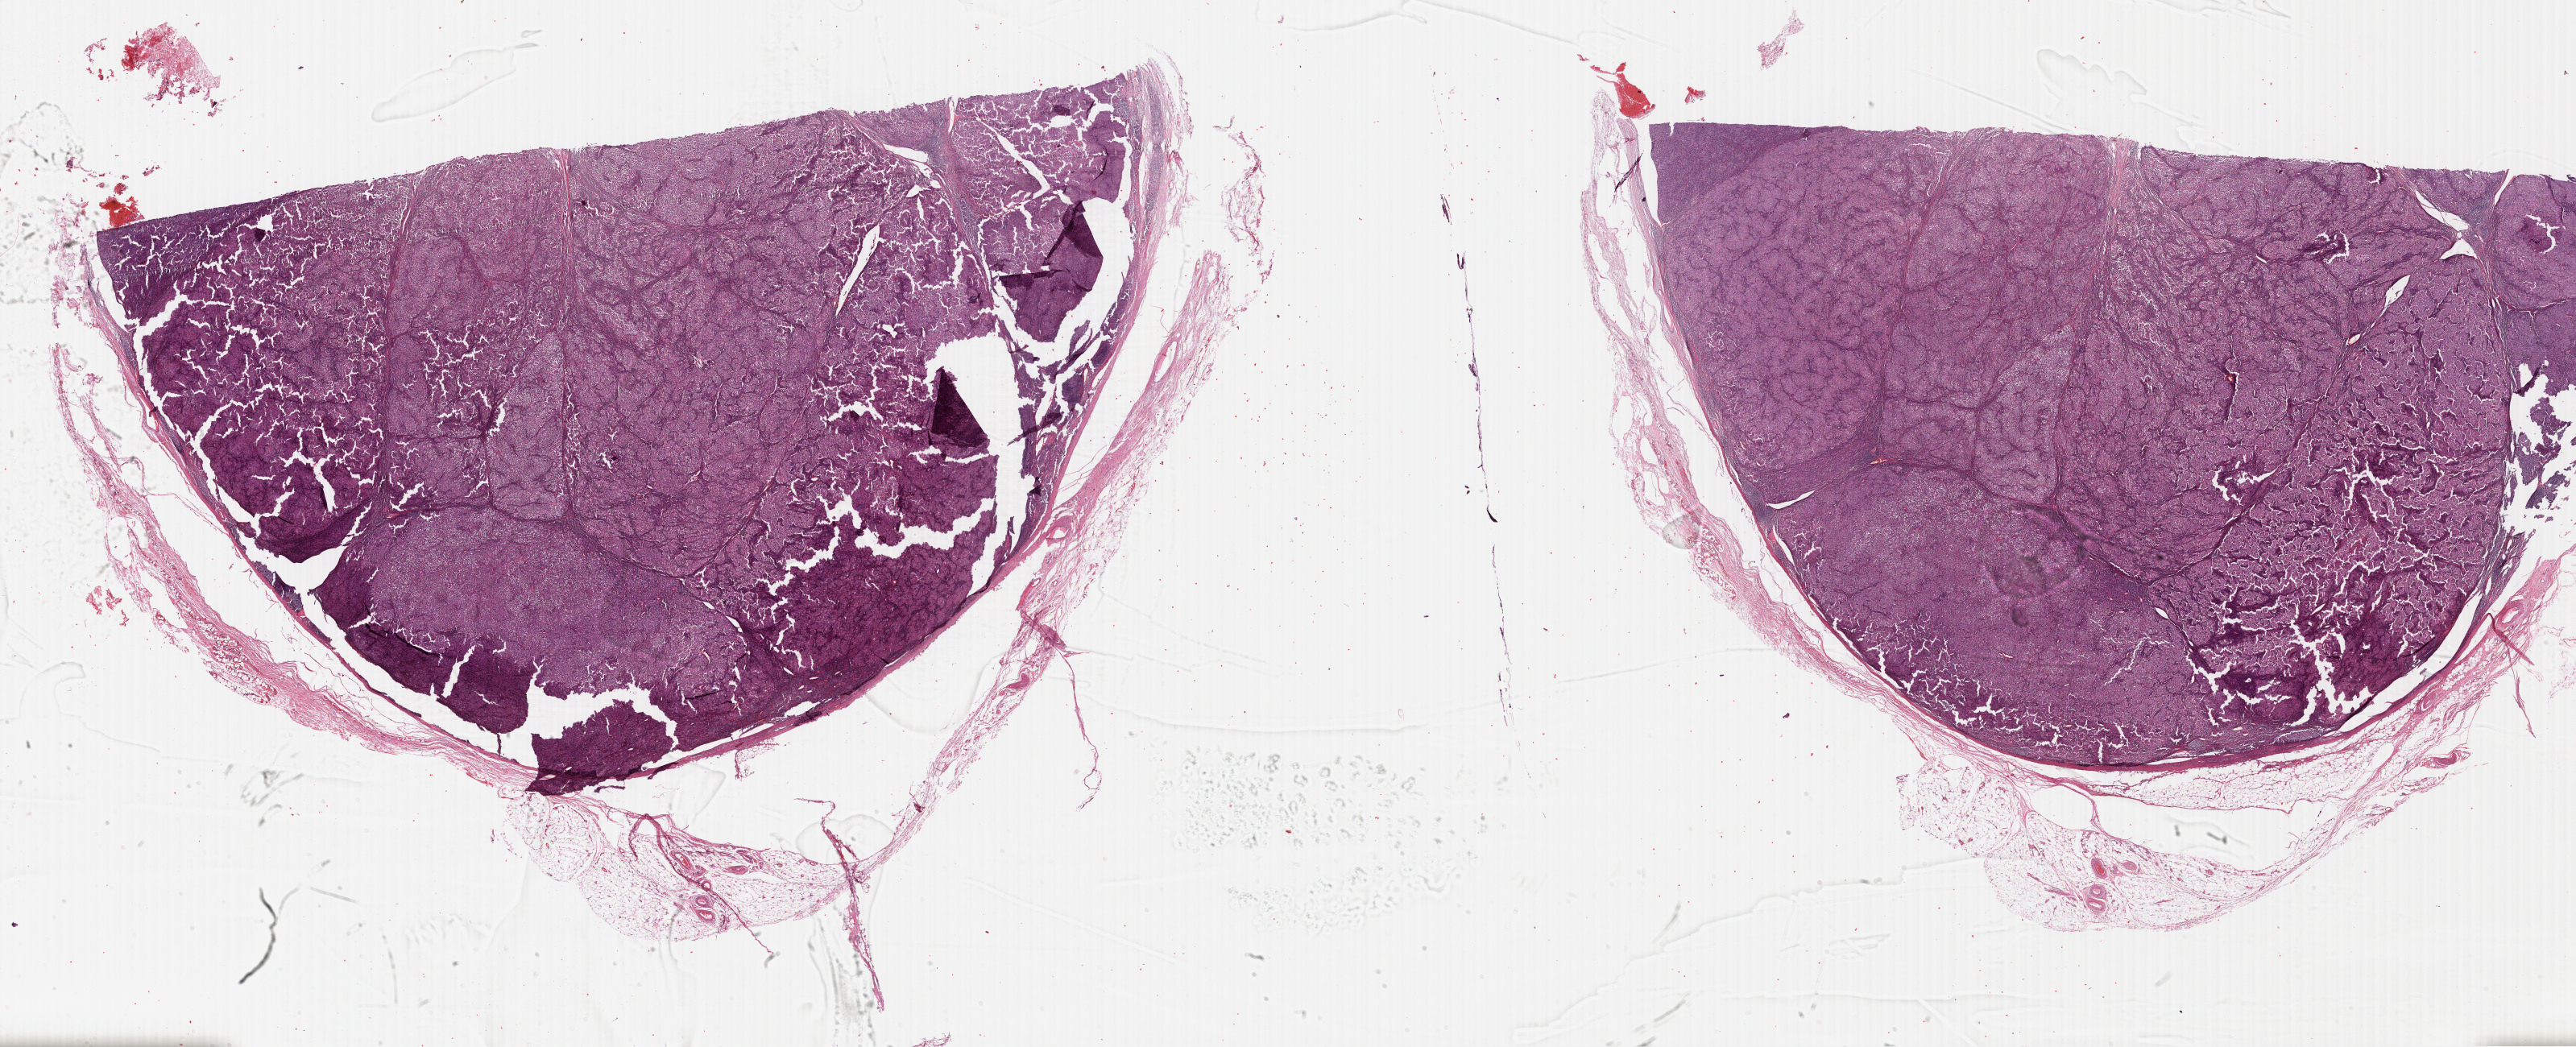
Hematoxylin and eosin (H&E) stained whole-slide image — shown as a low-resolution overview of the whole scanned area (about 50.3 x 20.4 mm). FFPE section. Metastatic tumour sample, sampled site: lymph node. Male patient; age at initial diagnosis 65 years.
* this section: metastatic tumour tissue
* patient diagnosis: Malignant melanoma, NOS